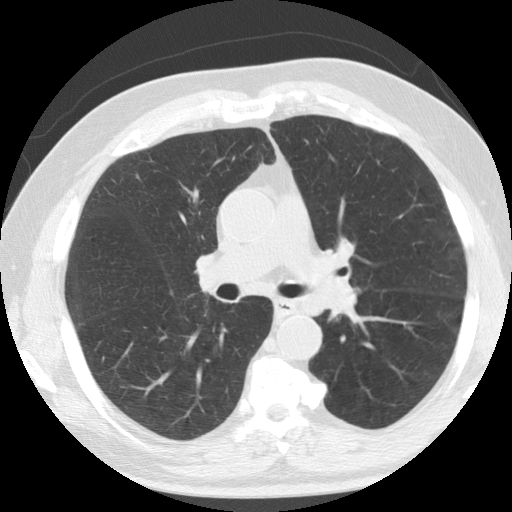
Low-dose screening chest CT, one axial slice; position 80 of 133 along the scan axis; reconstruction kernel STANDARD; lung window (W 1500 / L -600 HU); 2.5 mm slice thickness; 512 × 512 image matrix, field of view 342 × 342 mm.
Annotated regions visible in this slice (outlined manually by an expert reader):
- lesion 1 (tumor, upper lobe of left lung): bounding box (x1, y1, x2, y2) in pixels: (322, 276, 356, 314)